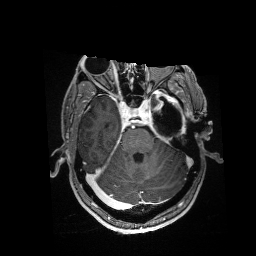
Brain MRI from a brain-tumour surgery series, one axial slice; position 112 of 176 along the scan axis; T1-weighted post-contrast; 256 × 256 image matrix, field of view 256 × 256 mm. From the clinical record (not read from this slice): histopathology: Glioblastoma; WHO grade: 4; IDH mutation: no; tumour location: Left Anterior/Superior Temporal.
Structures marked on this image (outlined manually by an expert reader):
- residual tumour: bounding box (x1, y1, x2, y2) in pixels: (155, 90, 182, 112)